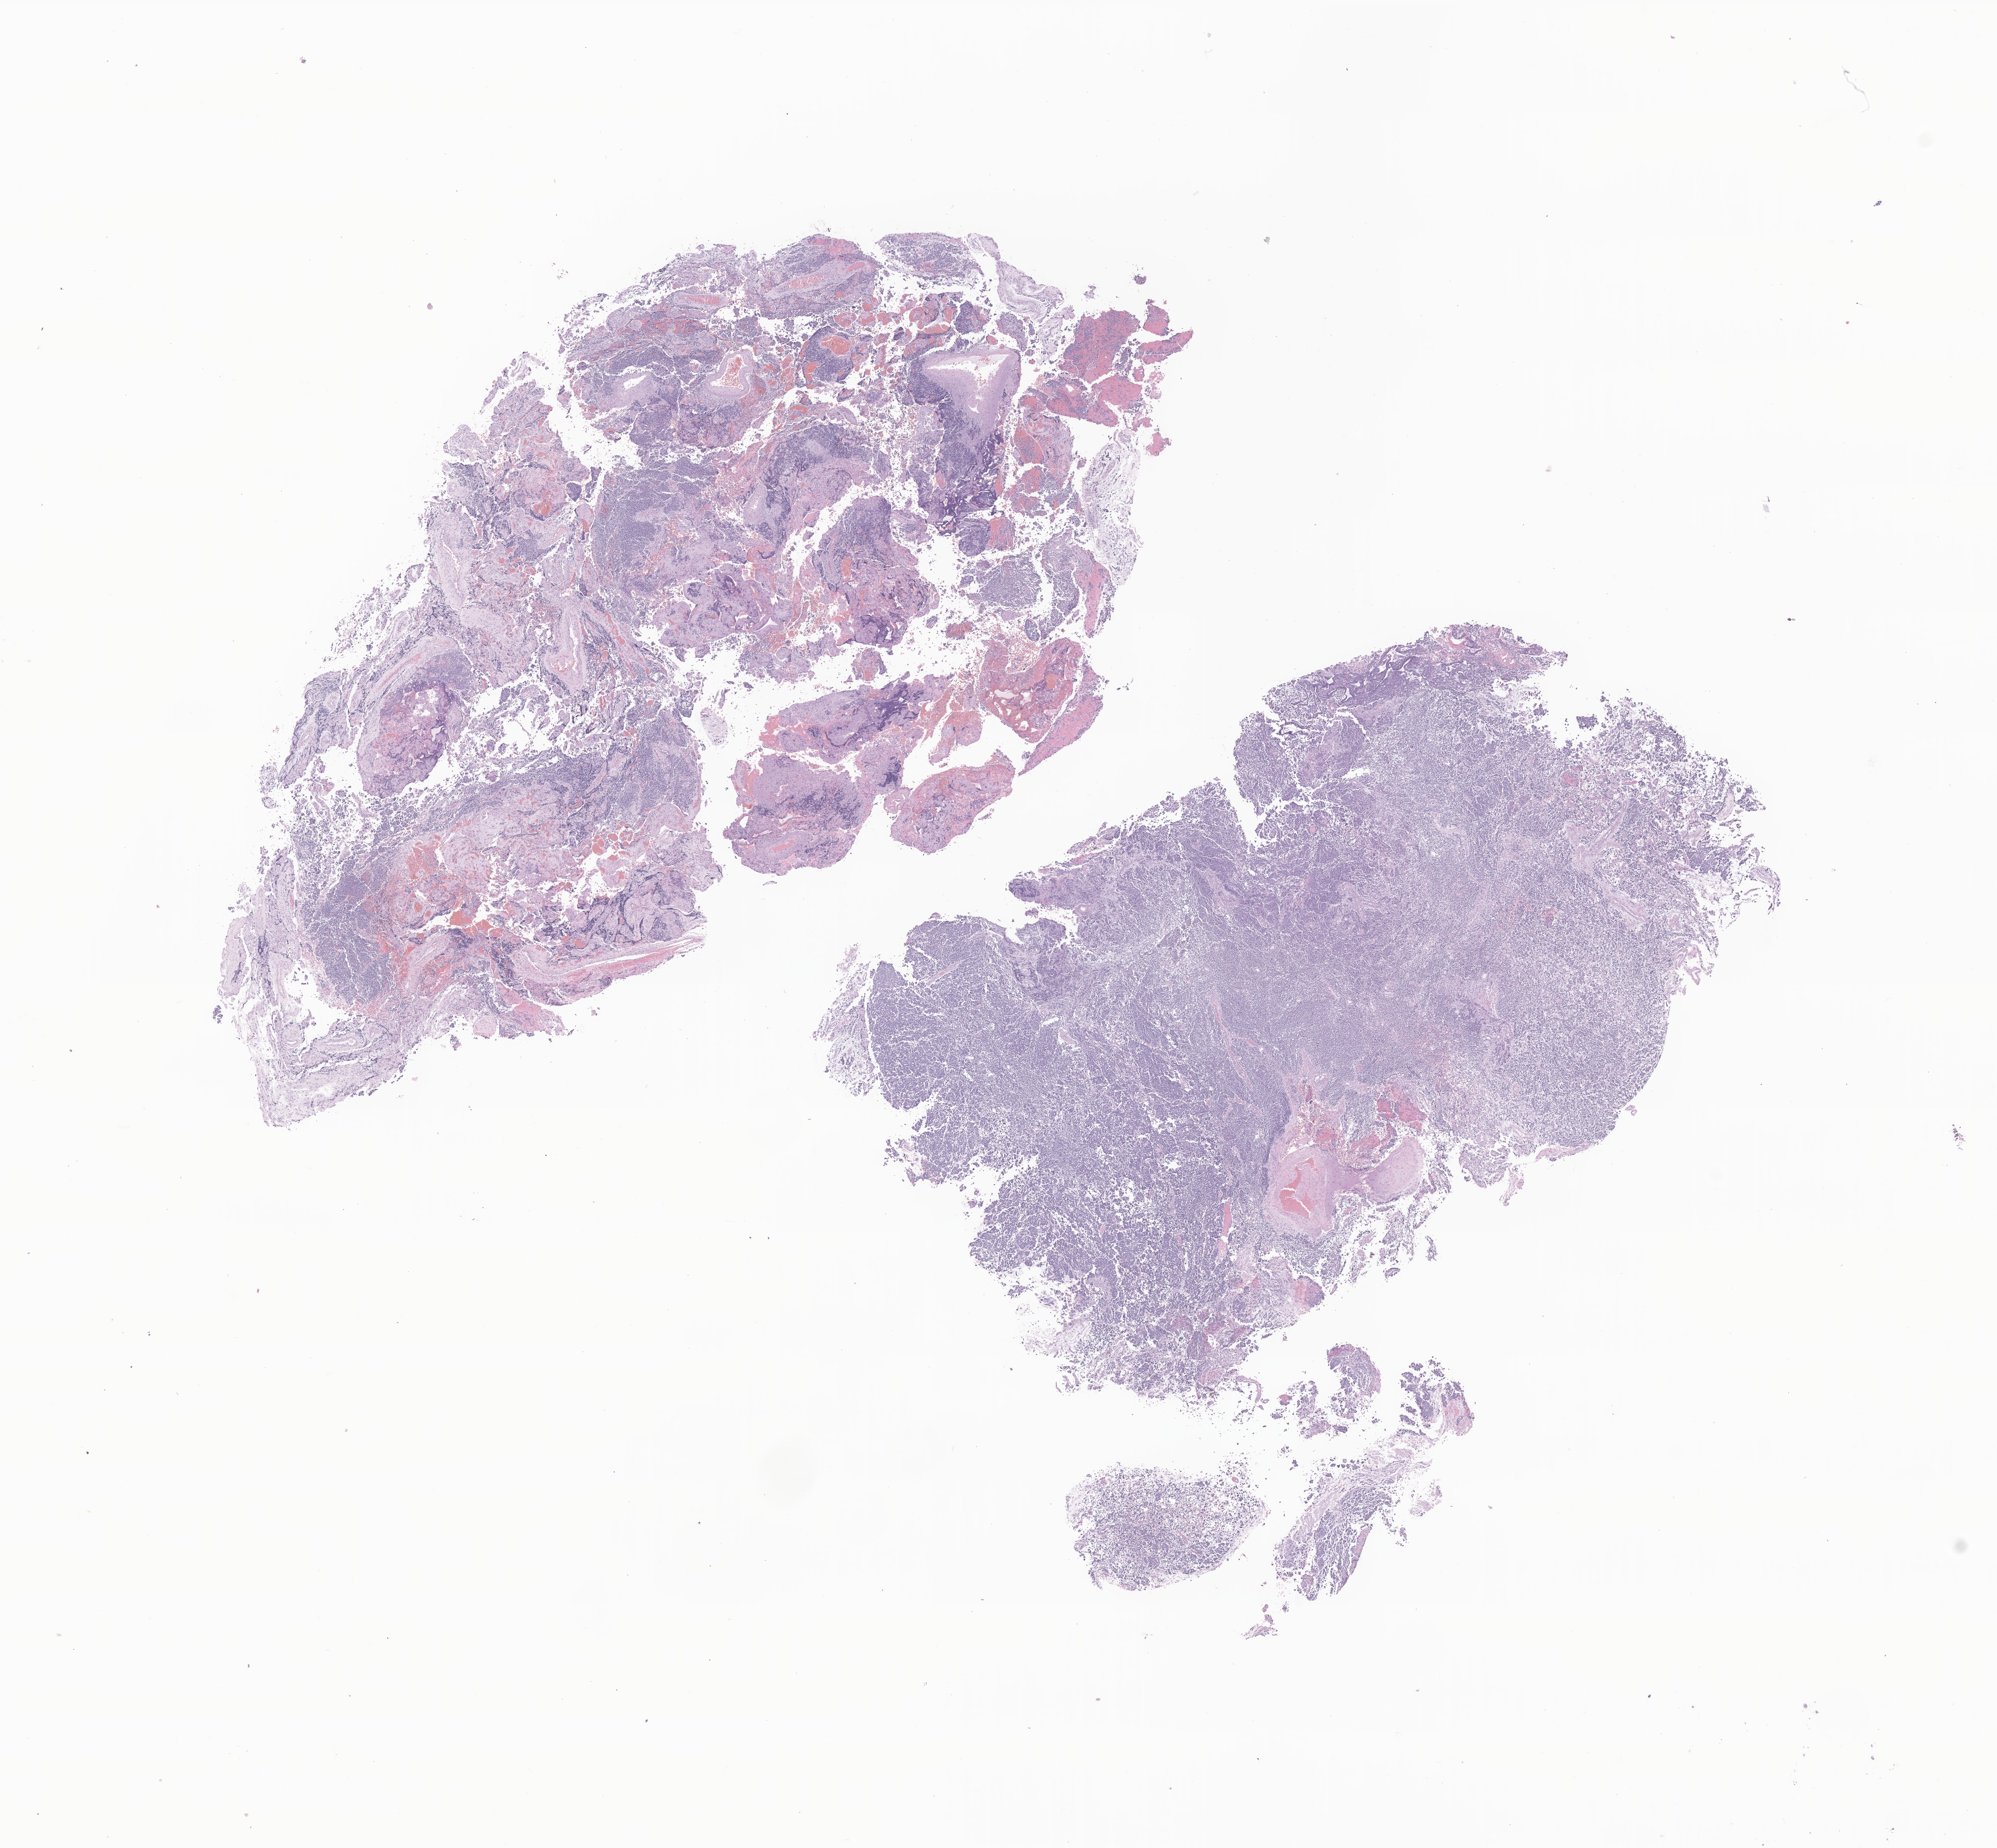
H&E whole-slide image of tumor tissue from the brain, a low-resolution overview of the entire scanned area, about 17.1 x 15.9 mm. Formalin-fixed paraffin-embedded section. Male patient, age 41 months (3 years 5 months).
• diagnosis (ICD-O-3 morphology term): Neoplasm, uncertain whether benign or malignant